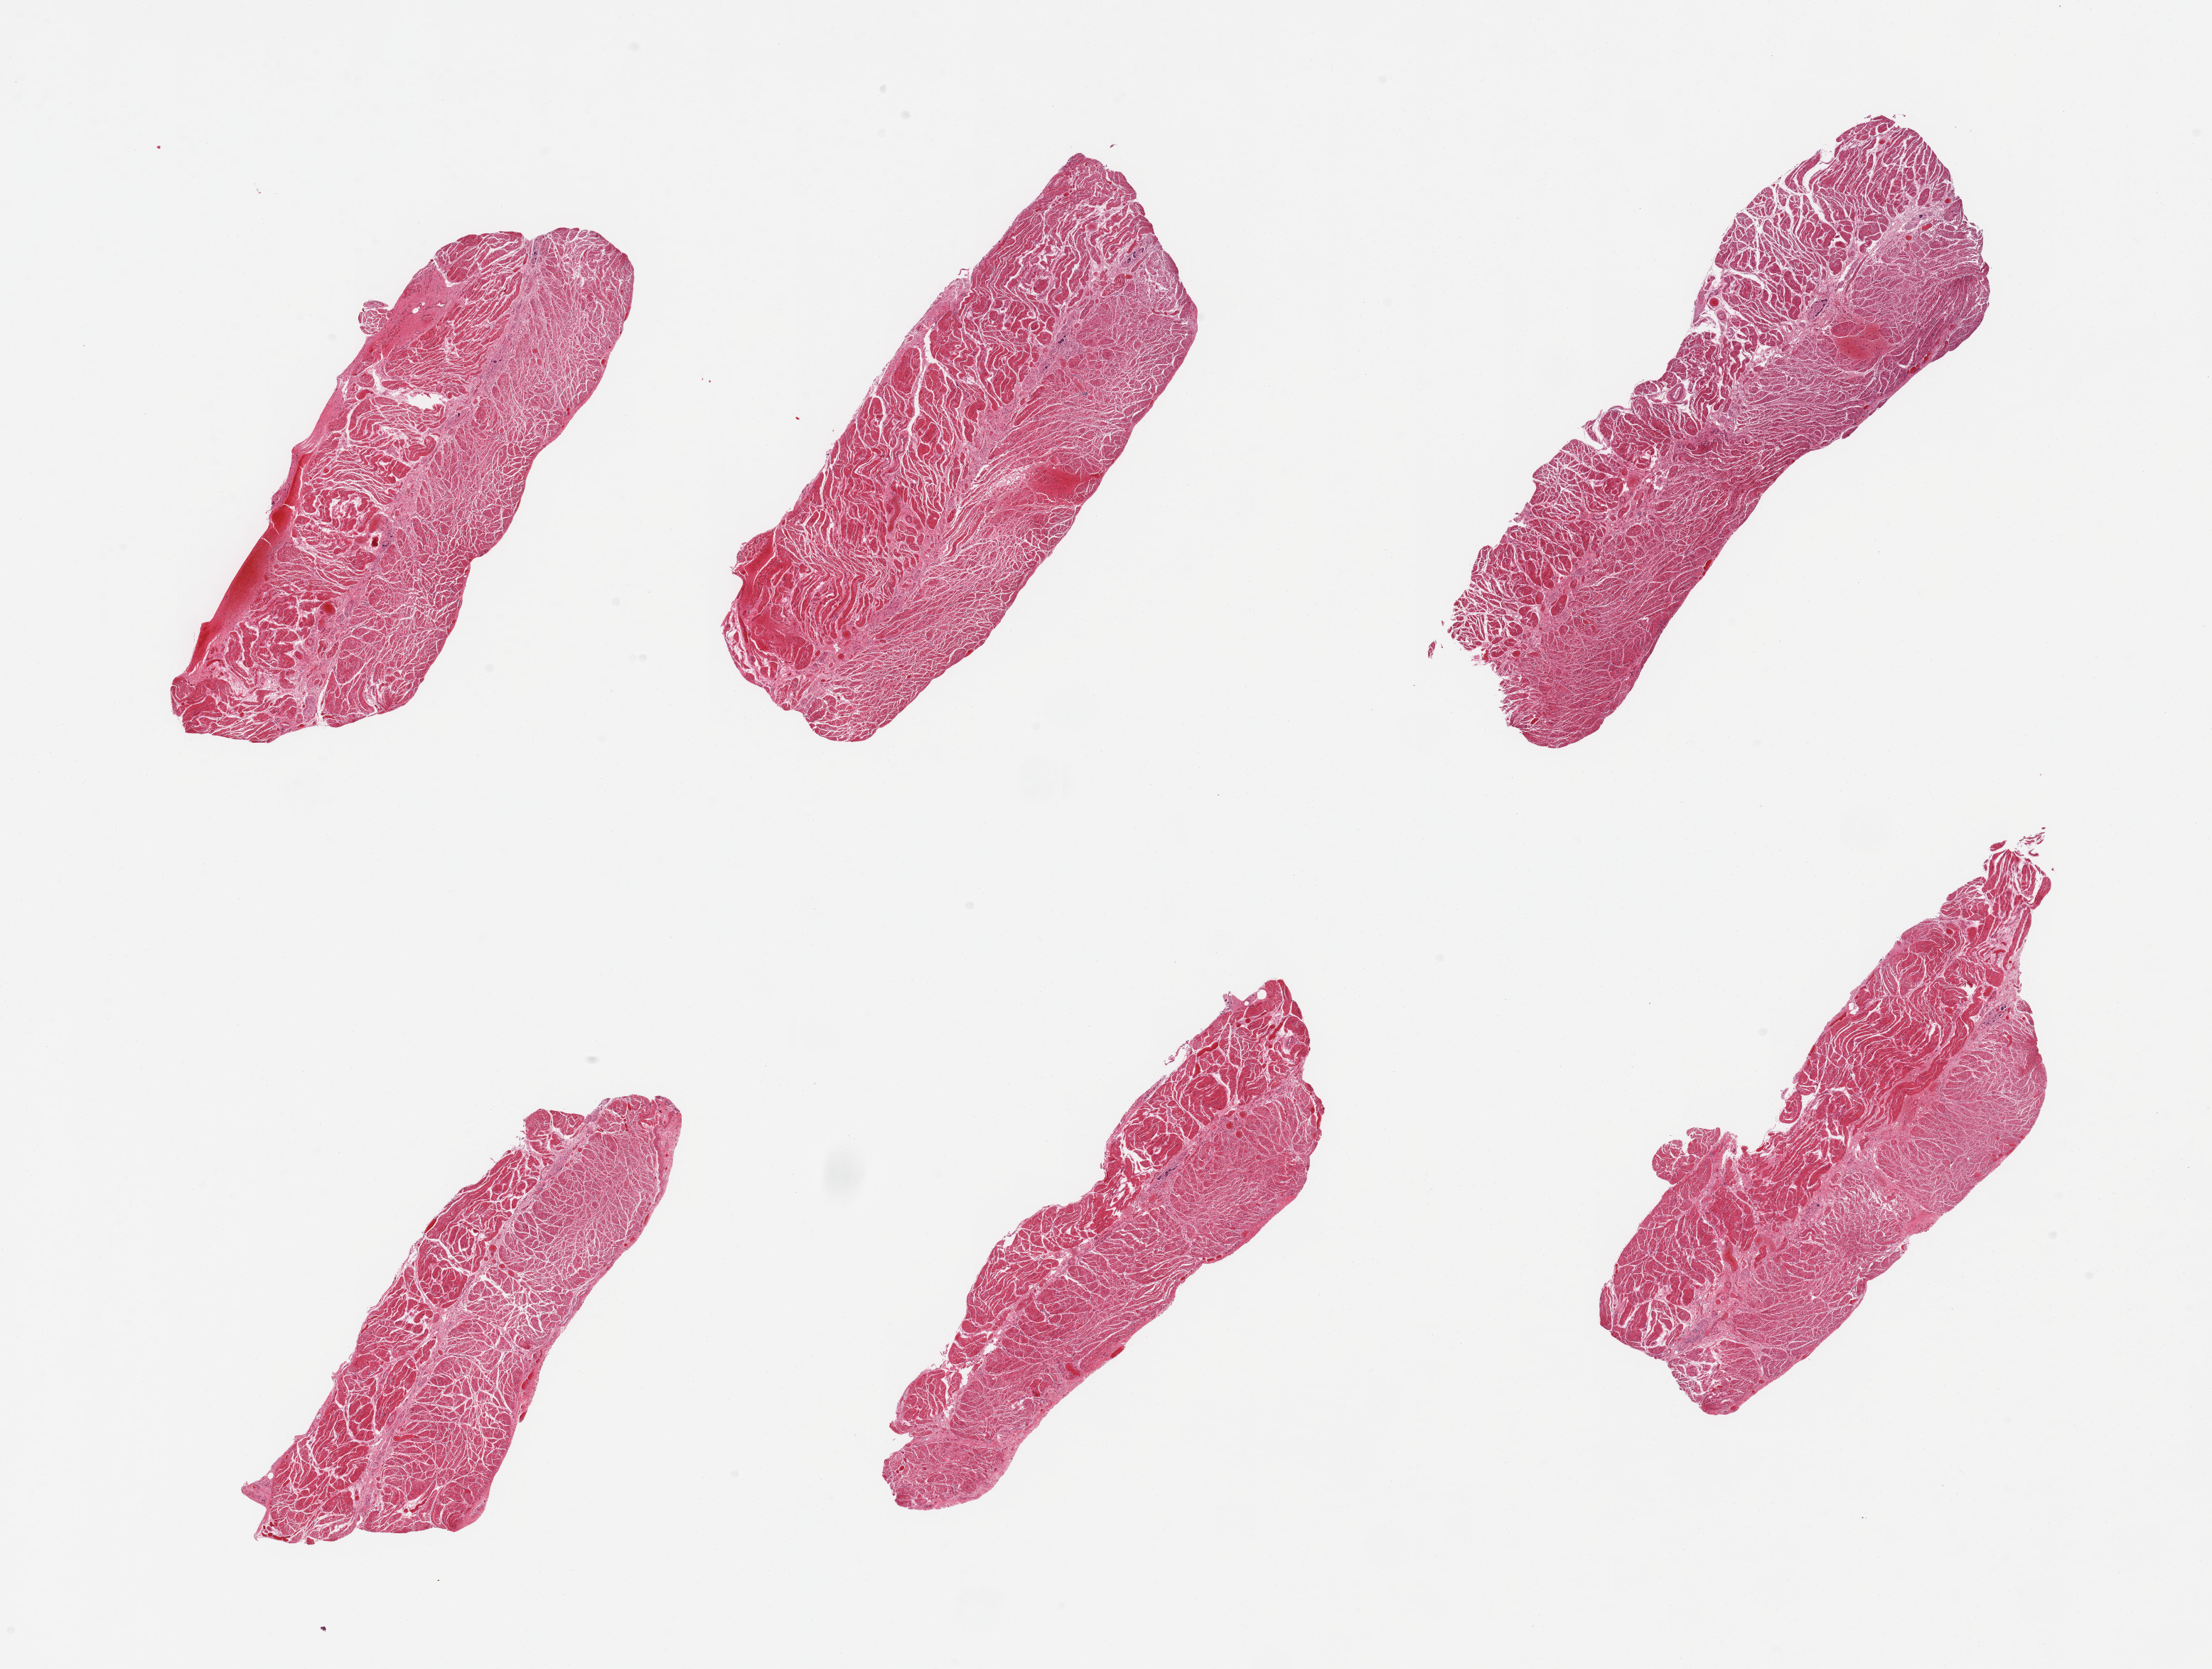
Whole-slide image, haematoxylin and eosin stain — shown as a low-resolution overview of the whole scanned area (about 24.6 x 18.6 mm), PAXgene-fixed, paraffin-embedded tissue, sampled site (target tissue): gastroesophageal junction, donor tissue sample. Donor: male.
Pathologist's review note for this sample: 6 pieces; target muscularis.